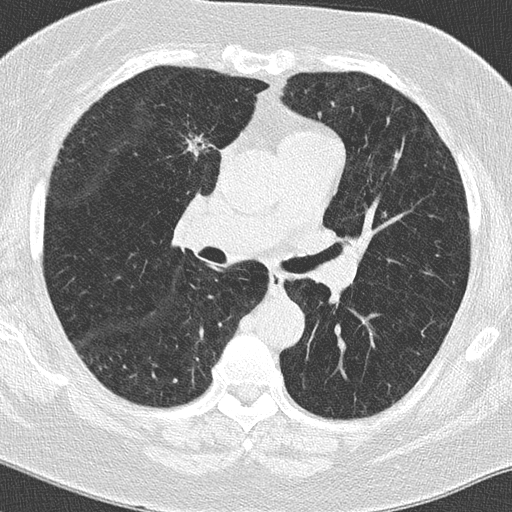
Axial slice from a low-dose chest CT screening exam, second annual screen, lung window (W 1500 / L -600 HU), 2 mm slice thickness, lung (sharp) reconstruction kernel (B50f), 512 × 512 image matrix. Female, age 62 years at enrolment. Current smoker at enrolment.
Expert-annotated lung lesion, box from (x=159, y=114) to (x=229, y=174) px. The screening reader recorded 2 non-calcified nodules or masses ≥4 mm on this exam (left lower lobe, right middle lobe); which of them this box marks is not recorded. Official screen result: positive, other. Lung cancer was diagnosed 396 days after this screen: adenocarcinoma, NOS, right upper lobe, moderately differentiated (G2), stage IA (AJCC 6th edition), 15 mm at pathology.